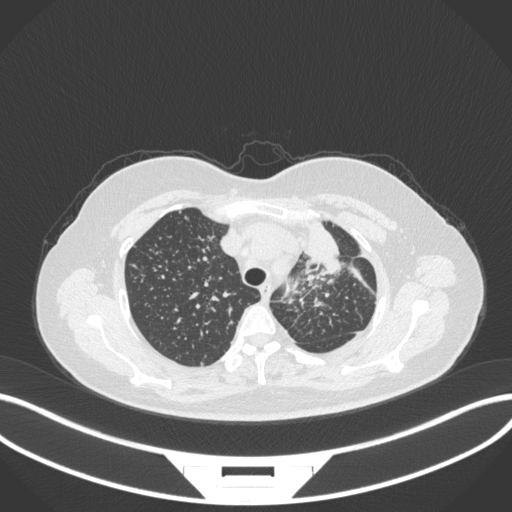
Chest CT, one axial slice; position 264 of 348 along the scan axis; reconstruction kernel B31f; 120 kVp; lung window (W 1500 / L -600 HU); 1 mm slice thickness; 512 × 512 image matrix, field of view 400 × 400 mm. Female patient, age 49 years. From the clinical record (not read from this slice): clinical TNM (as recorded): T1c N0 M1.
Outlined on this slice (rectangle marked by the reading radiologist):
- lung tumour (recorded histology: adenocarcinoma): bounding box [x1, y1, x2, y2] px = [299, 214, 348, 274]